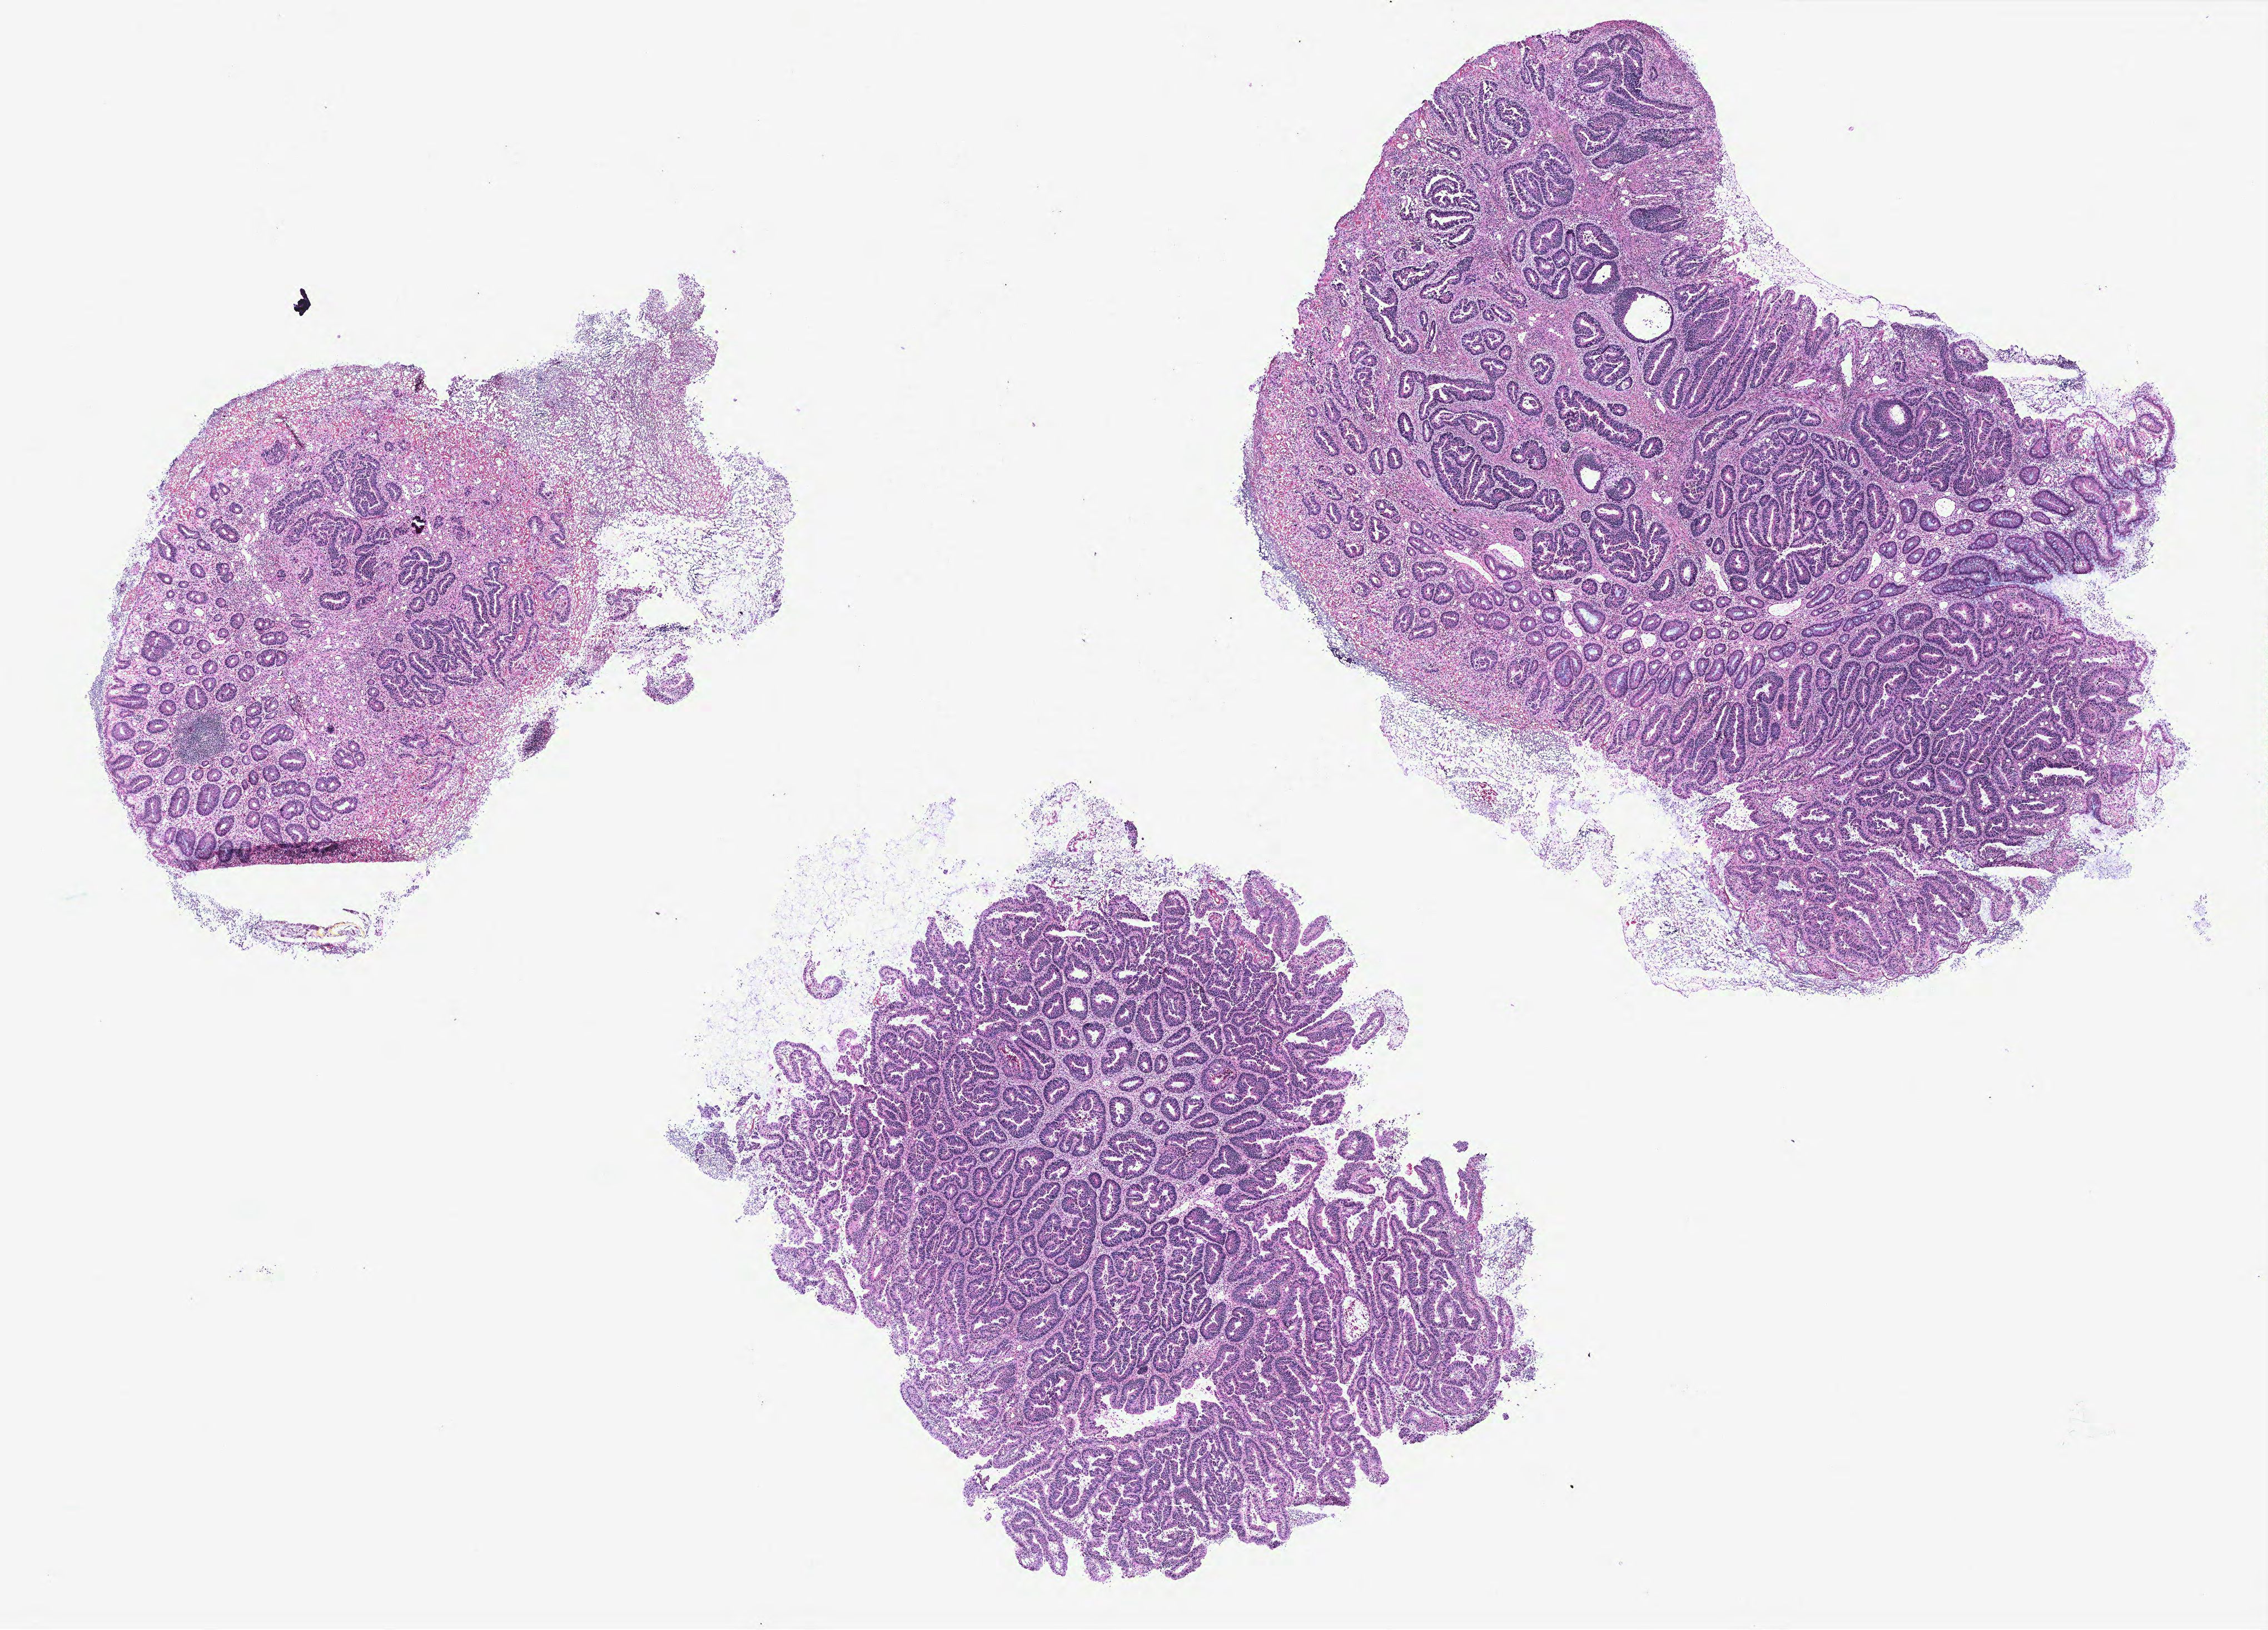
Digitized H&E tissue section (whole slide), shown as a low-resolution overview of the whole scanned area (about 16.3 x 11.7 mm); normal (non-tumour) tissue sample, colon. Patient: male, age 68 years.
* this section: normal (non-tumour) tissue from the same patient
* patient diagnosis: Adenocarcinoma, NOS